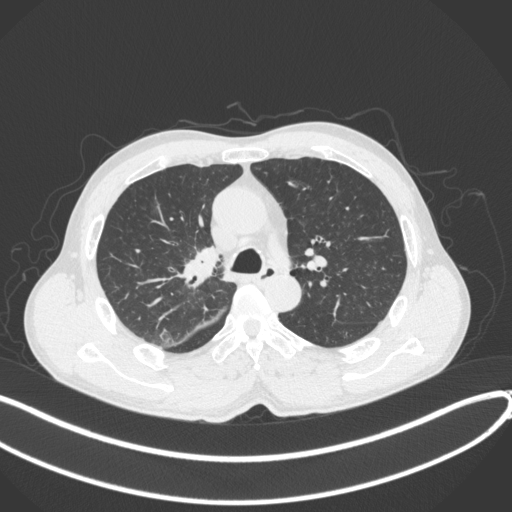
Chest CT, one axial slice. Slice 262 of 409 in the series (ordered by position). Lung window (W 1500 / L -600 HU). 1 mm slice thickness. 512 × 512 image matrix, field of view 400 × 400 mm. Patient: male, 53 years. Case-level facts recorded for this patient, not image findings: clinical TNM (as recorded): T1b N0 M0.
Annotated regions visible in this slice (rectangle marked by the reading radiologist):
- lung tumour (recorded histology: squamous cell carcinoma): bounding box <181,244,224,290> (left, top, right, bottom; pixels)